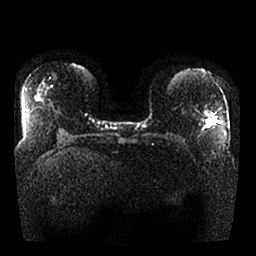
Breast MRI, one axial slice; position 15 of 25 along the scan axis; diffusion-weighted series; image 2 of 4 stored at this slice position (different b-values; order by instance number); 1.5 T; 256 × 256 image matrix. Female patient.
Outlined on this slice (outlined manually by an expert reader):
- tumour on diffusion-weighted imaging: box from (x=206, y=120) to (x=213, y=125) px